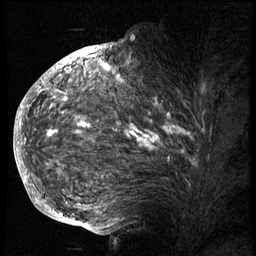
Breast MRI (dynamic contrast-enhanced), one sagittal slice; slice 45 of 74 in the series (ordered by position); 3 images stored at this slice position (order not interpretable as contrast timing); 1.5 T; TE 4.2 ms, TR 8.9 ms; 256 × 256 image matrix, field of view 200 × 200 mm. Patient: female, 57 years. Case-level facts recorded for this patient, not image findings: setting: breast cancer imaged before/during neoadjuvant chemotherapy; receptor status: HER2-positive.
Outlined on this slice (semi-automatic segmentation, software-assisted and operator-edited):
- analysis volume of interest (the breast-tissue region the enhancement analysis was run in; not a lesion): bounding box <40,62,242,175> (left, top, right, bottom; pixels)
- tumour enhancement mask (voxels above the 140 % enhancement threshold inside the analysis volume of interest): <42,63,183,150>